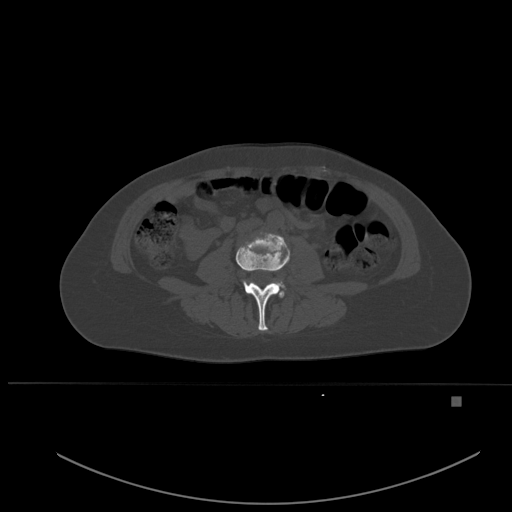
CT including the spine, one axial slice; slice 188 of 651 in the series (ordered by position); bone window (W 1800 / L 400 HU); 1.5 mm slice thickness; 512 × 512 image matrix, field of view 443 × 443 mm. Female patient, age 49 years. From the clinical record (not read from this slice): primary cancer: breast; vertebrae with lytic lesions (as recorded): L3, T12, L4.
Structures marked on this image (semi-automatically segmented with operator editing):
- L3 vertebra: bounding box <236,233,290,331> (left, top, right, bottom; pixels)
- L4 vertebra: <273,282,284,287>